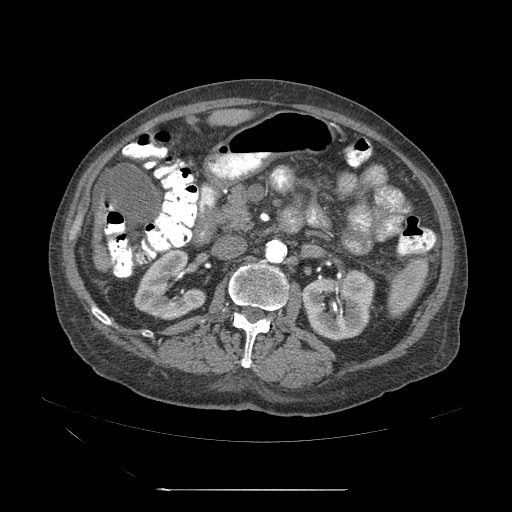
Contrast-enhanced abdominal CT (liver protocol), one axial slice; slice 10 of 71 in the series (ordered by position); reconstruction kernel STANDARD; 120 kVp; soft-tissue window (W 400 / L 40 HU); 2.5 mm slice thickness; 512 × 512 image matrix, field of view 440 × 440 mm. Case-level facts recorded for this patient, not image findings: diagnosis: hepatocellular carcinoma (patient treated with transarterial chemoembolisation; whether this scan precedes or follows treatment is not stated here); TNM stage (as recorded): Stage-II; Child-Pugh class: A; tumour size: 1 cm.
Outlined on this slice (semi-automatic segmentation, software-assisted and operator-edited):
- abdominal aorta: bounding box (x1, y1, x2, y2) in pixels: (264, 239, 286, 264)